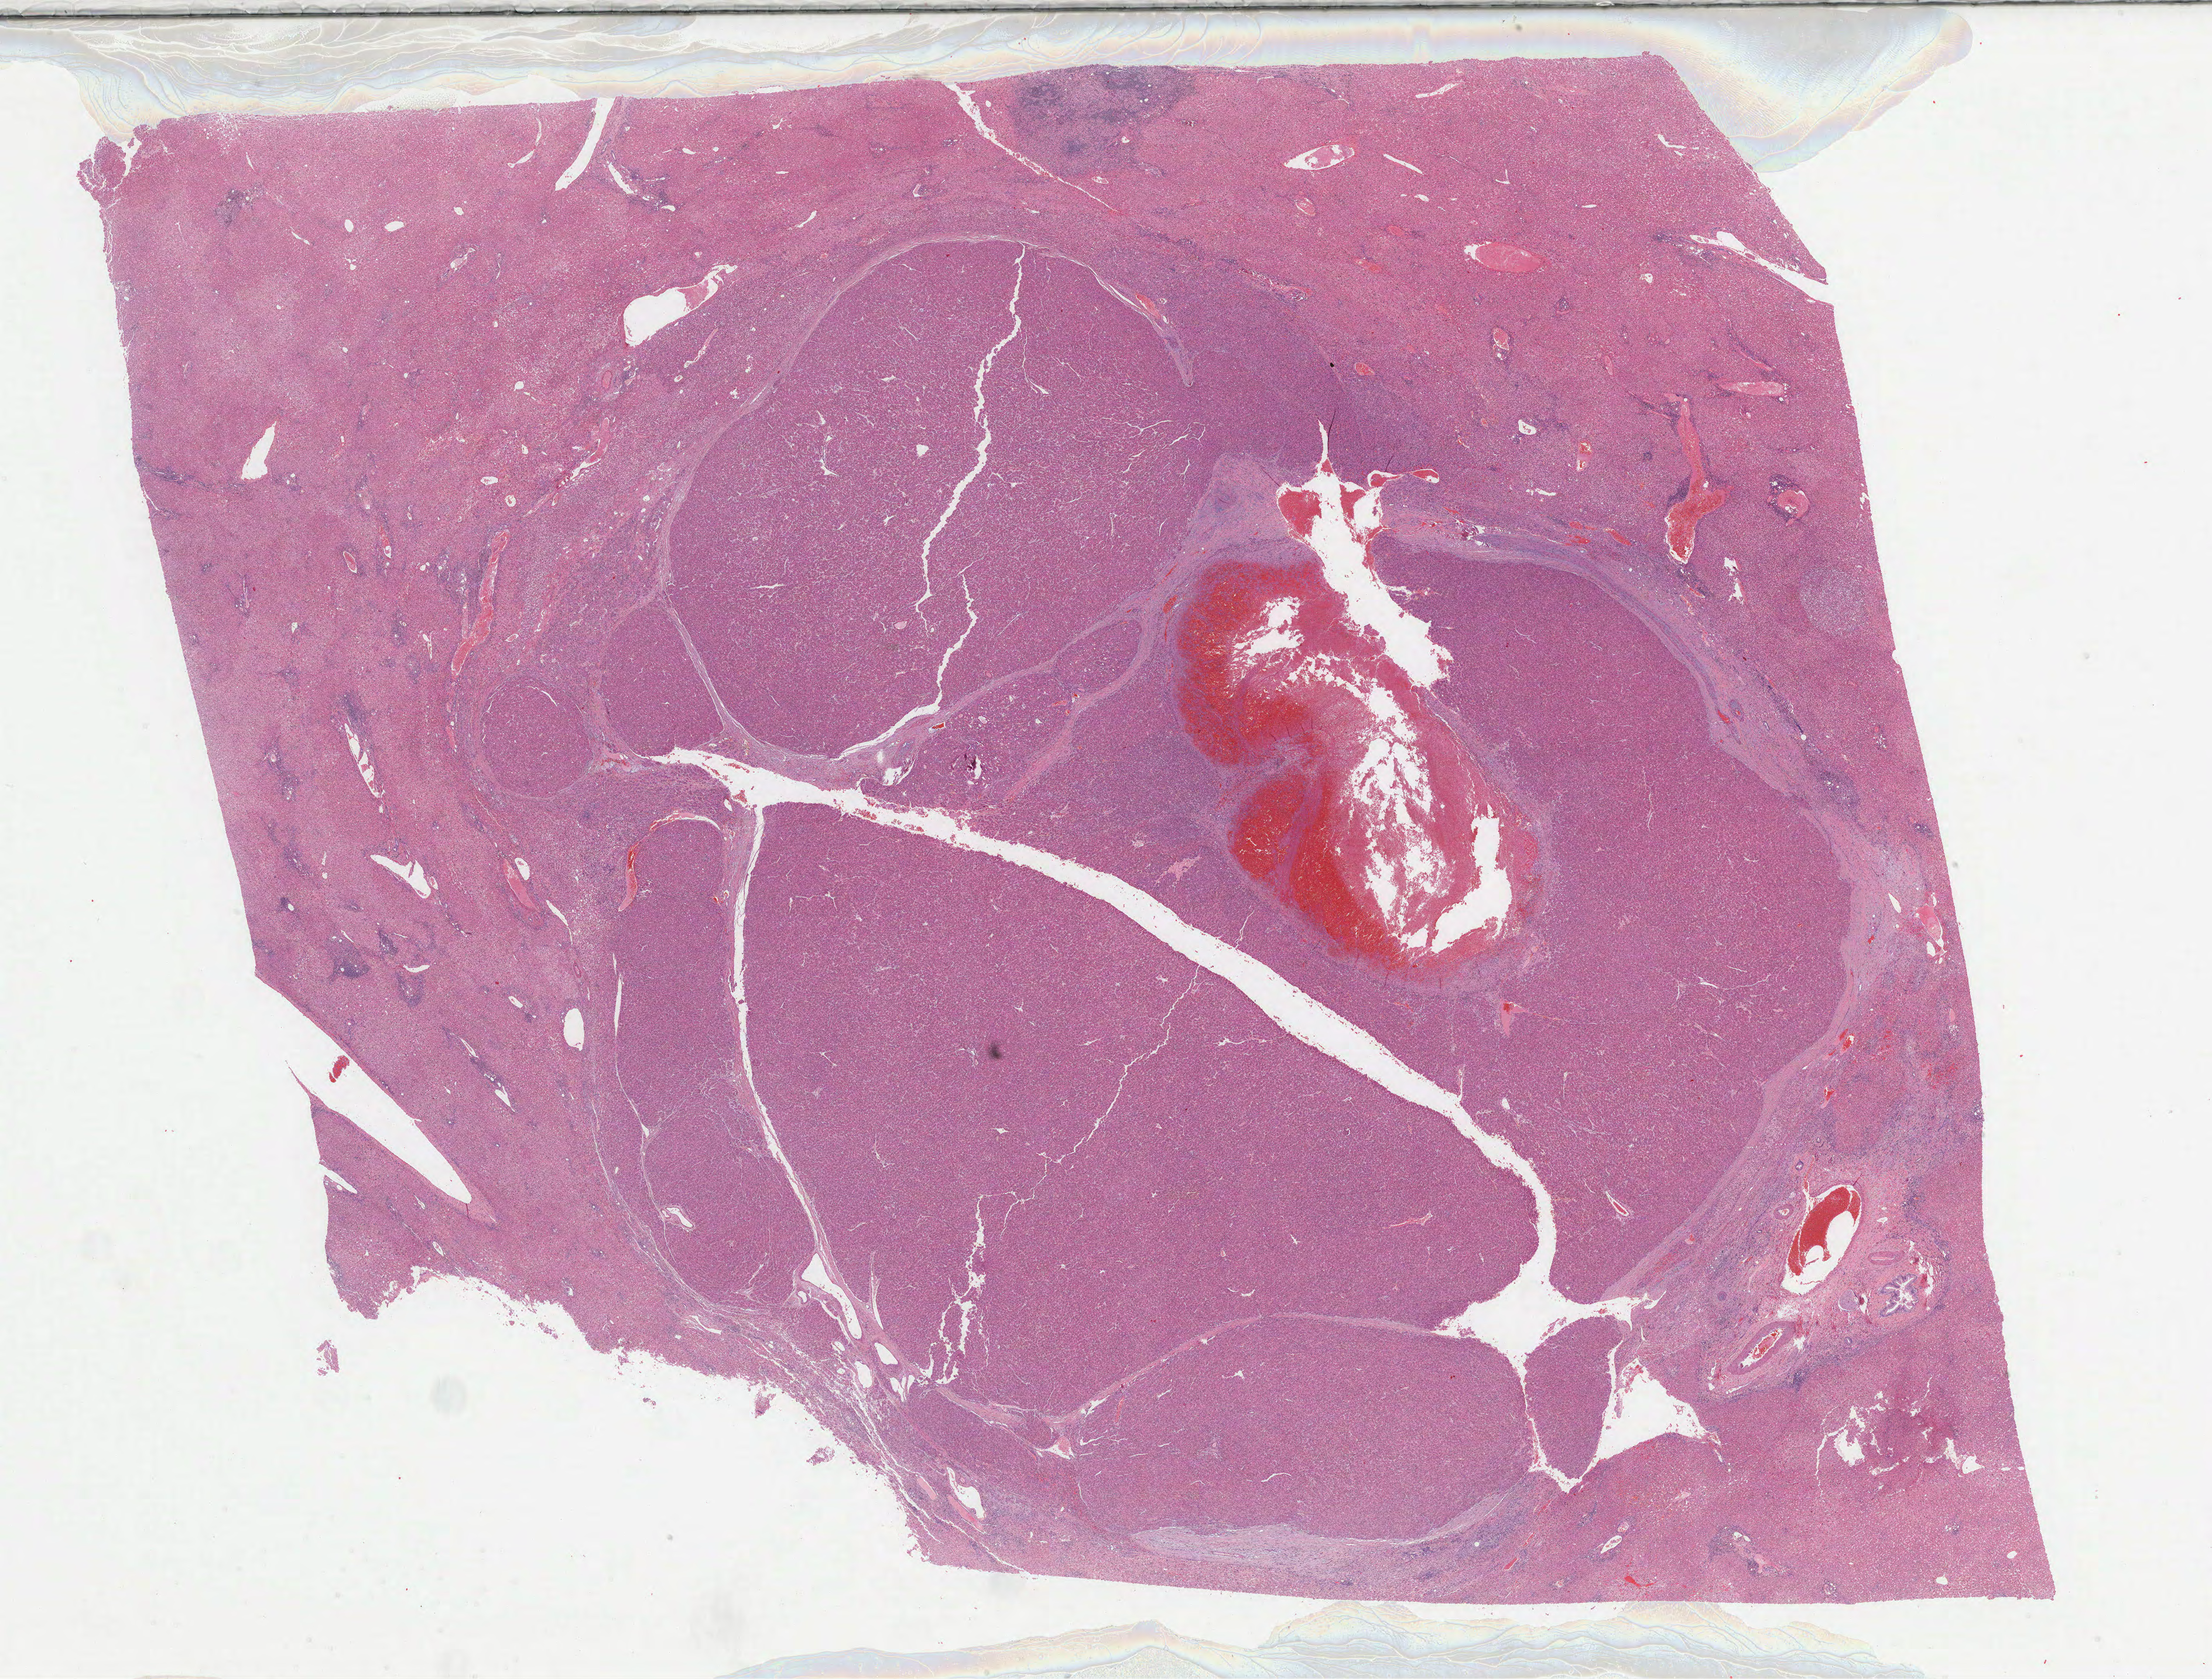
Digitized Hematoxylin and eosin (H&E) stained tissue section (whole slide) — shown as a low-resolution overview of the whole scanned area (about 30.5 x 23.2 mm, slide scanned at 40x), FFPE section, liver, primary tumour sample. Male, age 68 years at initial diagnosis. Histologic grade: G2 (moderately differentiated).
Diagnosis: Hepatocellular carcinoma, NOS. AJCC pathologic stage: I (7th edition).